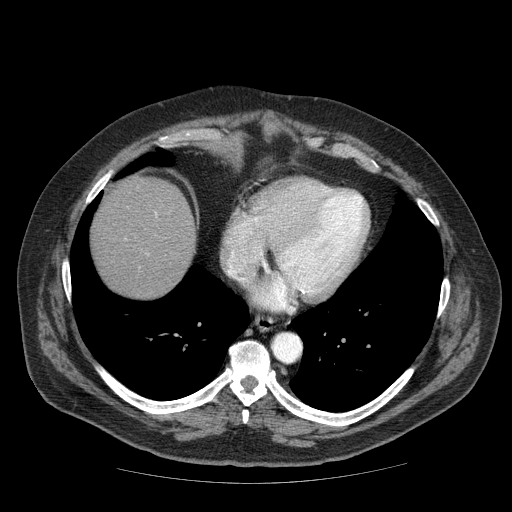
Contrast-enhanced abdominal CT (liver protocol), one axial slice; position 67 of 85 along the scan axis; 120 kVp; soft-tissue window (W 400 / L 40 HU); 2.5 mm slice thickness; 512 × 512 image matrix, field of view 420 × 420 mm. Case-level facts recorded for this patient, not image findings: diagnosis: hepatocellular carcinoma (patient treated with transarterial chemoembolisation; whether this scan precedes or follows treatment is not stated here); TNM stage (as recorded): Stage-IIIA; Child-Pugh class: A; tumour size: 7 cm.
Structures marked on this image (semi-automatic segmentation, software-assisted and operator-edited):
- liver parenchyma outside the tumour (the mass and vessels are separate outlines, so this box may not span the whole liver): bounding box <90,176,196,298> (left, top, right, bottom; pixels)